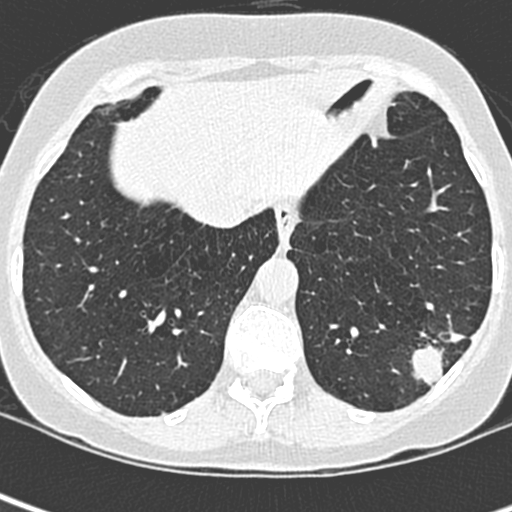
Low-dose screening chest CT, one axial slice. Slice 71 of 252 in the series (ordered by position). Lung window (W 1500 / L -600 HU). 1.3 mm slice thickness. 512 × 512 image matrix, field of view 271 × 271 mm.
Outlined on this slice (outlined manually by an expert reader):
- lesion 1 (tumor, lower lobe of left lung): box from (x=410, y=328) to (x=466, y=387) px